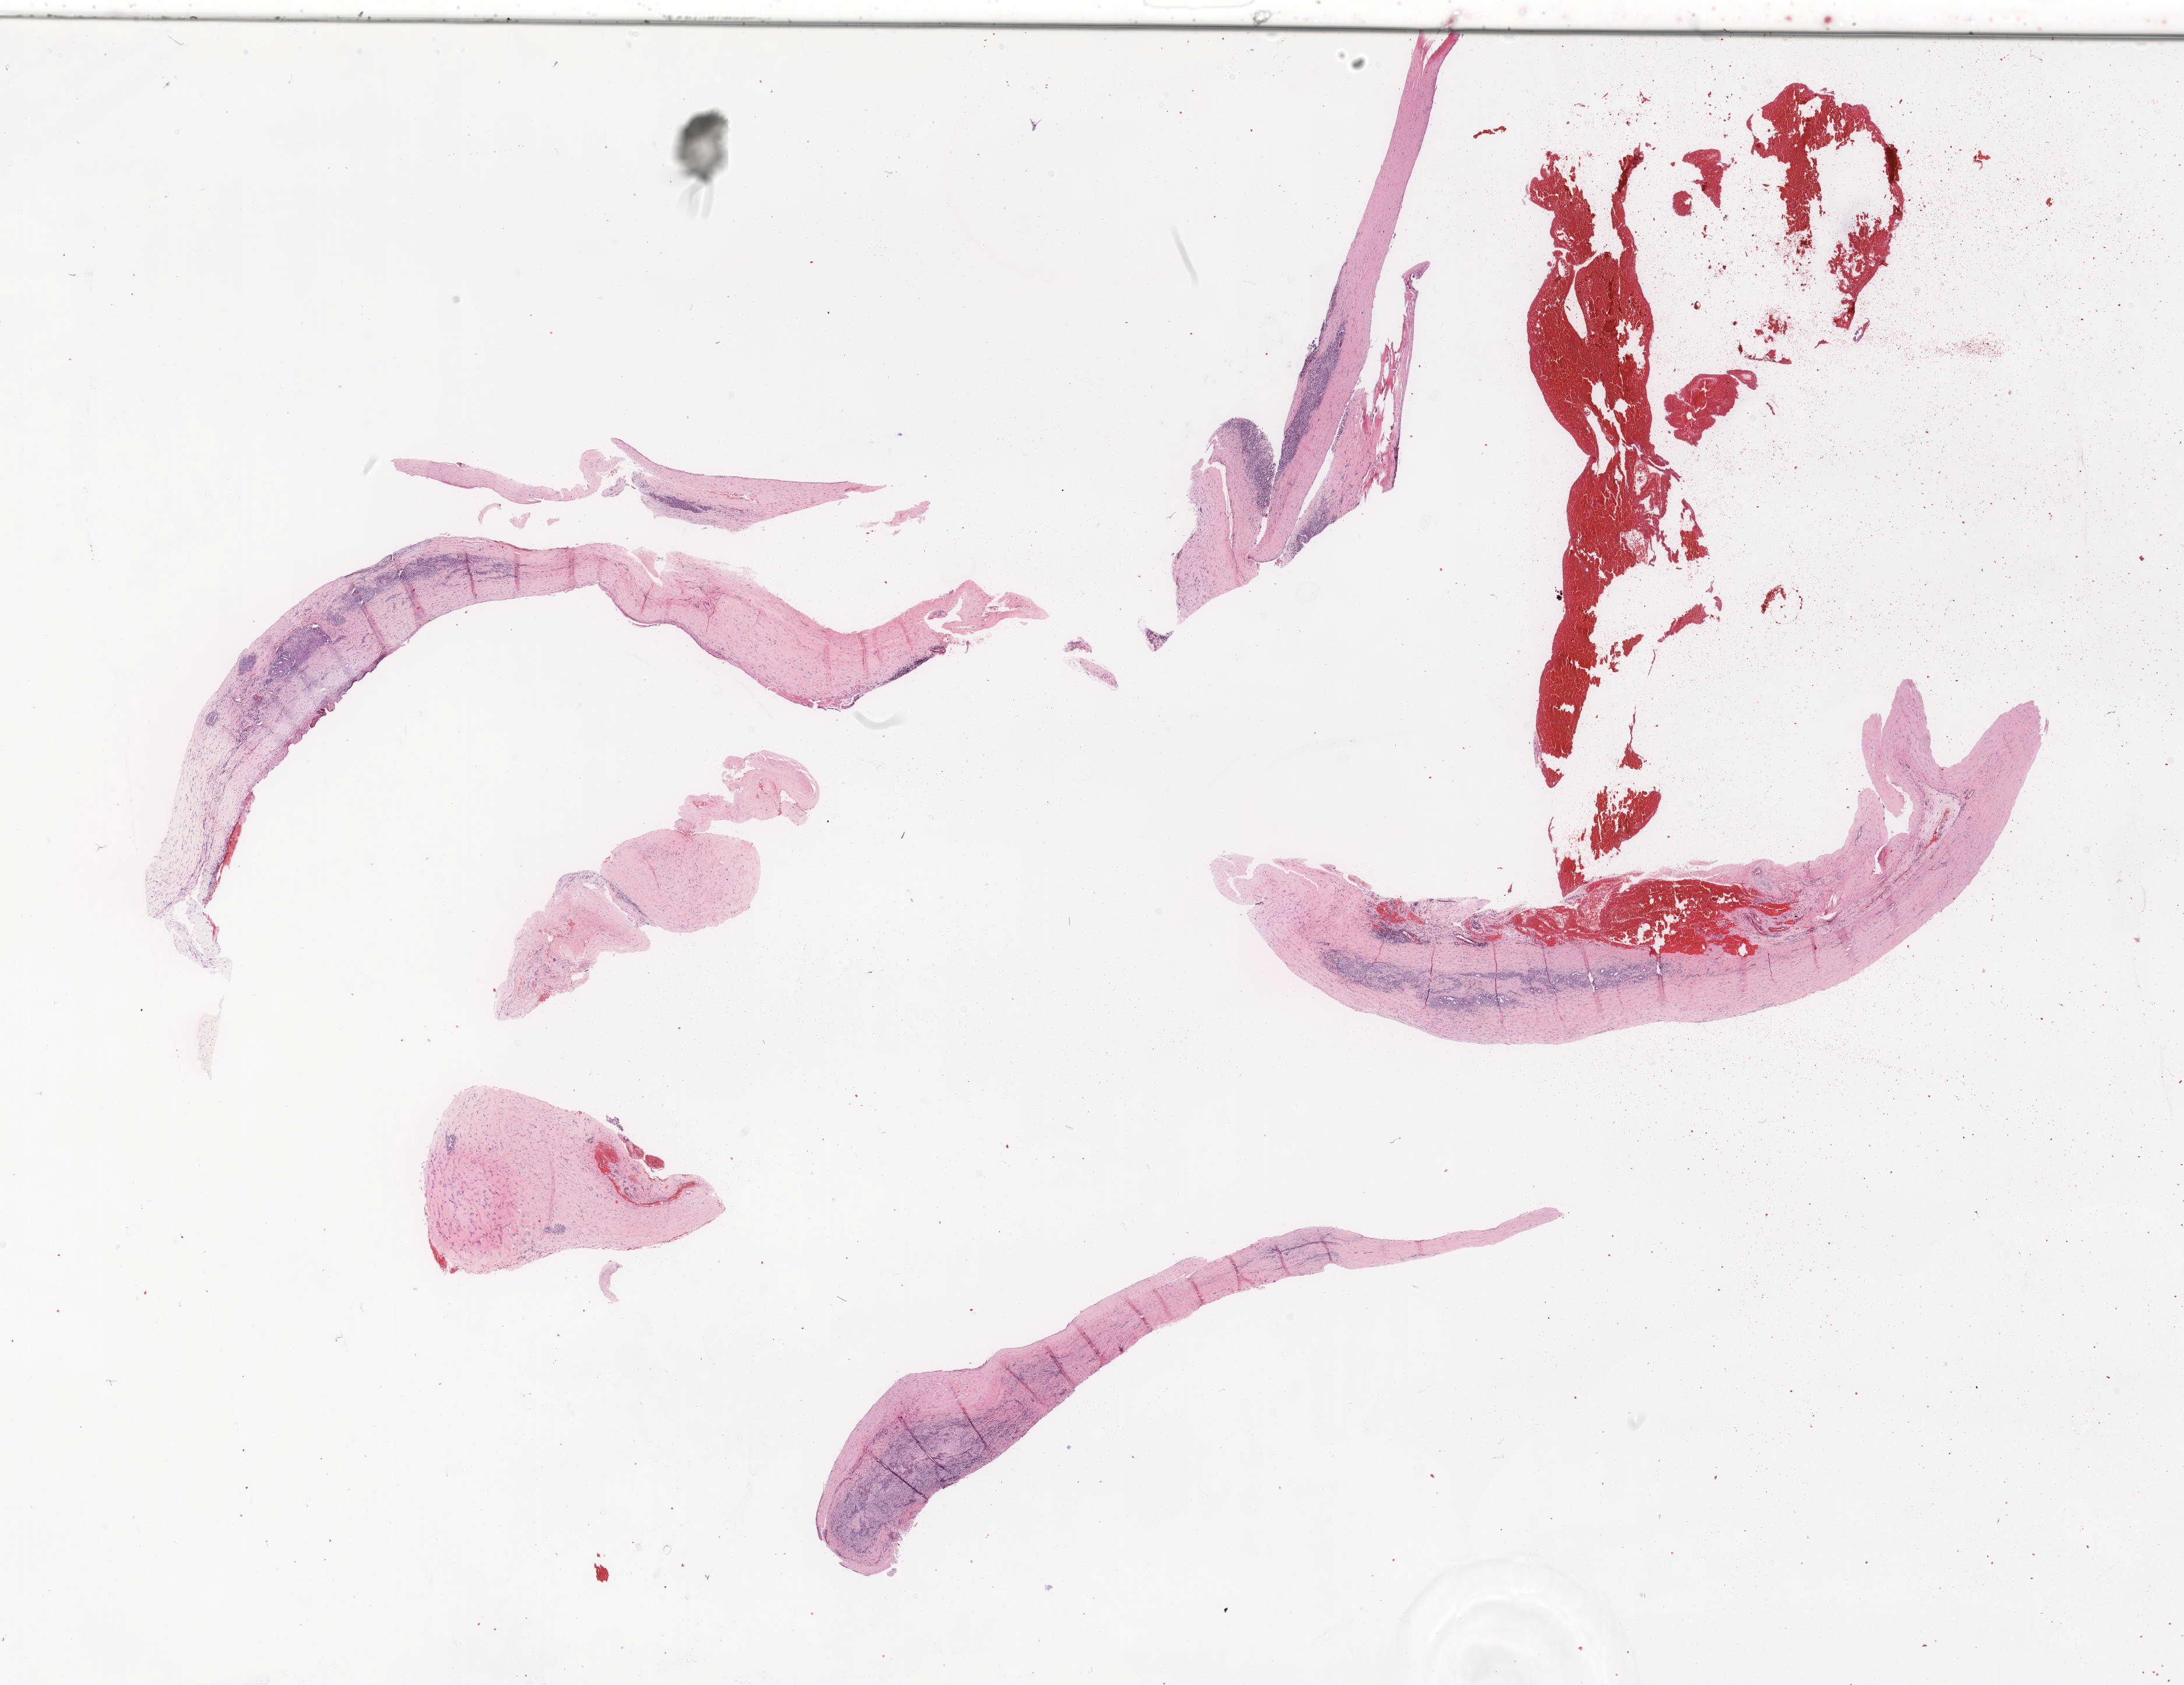
Whole-slide histology image, H&E, a low-resolution overview of the entire scanned area, about 30.1 x 23.2 mm (from a 20x scan), formalin-fixed paraffin-embedded (FFPE) diagnostic section, primary tumour sample from the mesothelium. Female, age 64 years at initial diagnosis.
- histologic diagnosis: Epithelioid mesothelioma, malignant (pleura, NOS)
- TNM: T4 NX M0
- AJCC pathologic stage: IV